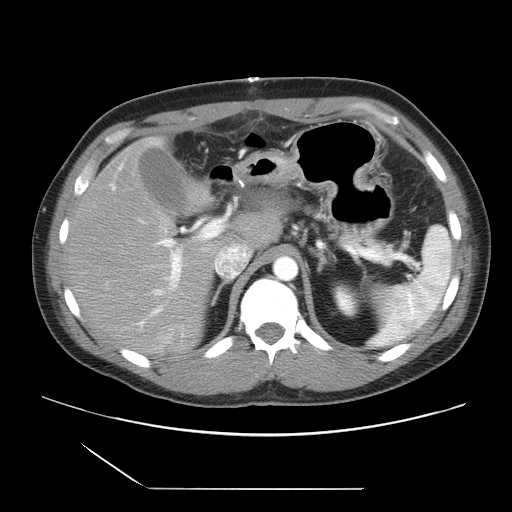
Contrast-enhanced abdominal CT, one axial slice. Position 17 of 39 along the scan axis. 120 kVp. Intravenous contrast given. Soft-tissue window (W 400 / L 40 HU). 512 × 512 image matrix, field of view 395 × 395 mm. Male patient, age 39 years. From the clinical record (not read from this slice): diagnosis: colorectal cancer liver metastases, imaged before liver resection; multiple liver metastases: yes; largest metastasis: 1.3 cm; disease in both lobes: no.
Structures marked on this image (outlined manually by an expert reader):
- hepatic veins: bounding box <215,245,250,278> (left, top, right, bottom; pixels)
- liver: <69,138,281,357>
- planned liver remnant (the part of the liver to remain after resection): <121,139,282,248>
- portal vein (with intrahepatic branches): <109,183,223,332>